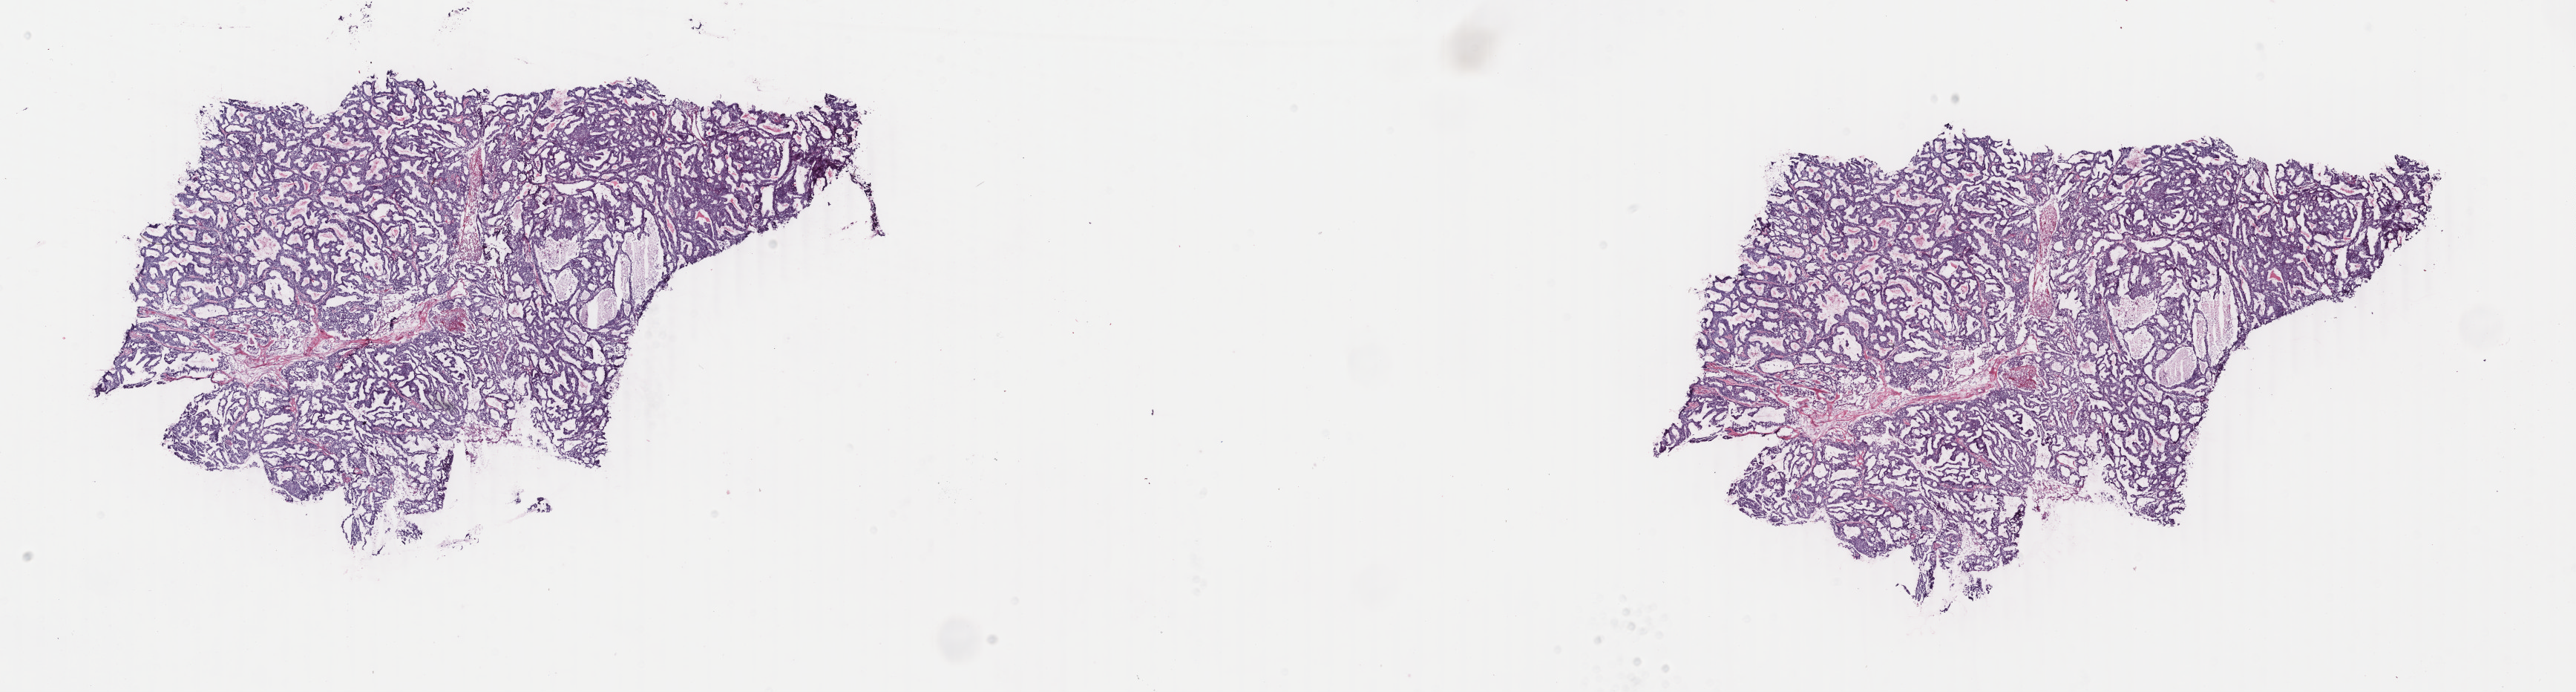
H&E-stained whole-slide image — shown as a low-resolution overview of the whole scanned area (about 27.6 x 7.4 mm, acquisition: 40x scan). Frozen section. Uterus, primary tumour sample. Patient: female, age at initial diagnosis 78 years. Histologic grade: G1 (well differentiated). Composition of this section per pathologist review: tumour cells 90%, tumour nuclei 94%, normal cells 0%, stromal cells 7%, necrosis 3%. Inflammatory infiltration, as recorded: lymphocyte infiltration 1%, monocyte infiltration 1%, neutrophil infiltration 1%.
Diagnosis: Endometrioid adenocarcinoma, NOS (endometrium). Lymph nodes positive (case pathology): 0 of 8 examined. FIGO stage: IIIA.